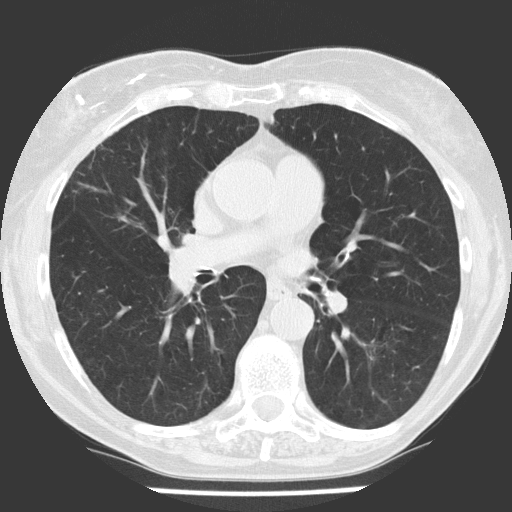
Axial slice from a low-dose chest CT screening exam. Baseline annual screen. Lung window (W 1500 / L -600 HU). Slice 70 of 147 in the series. Female, age 68 years at enrolment.
Expert reader's lesion annotation, bounding box [x1, y1, x2, y2] px = [353, 328, 400, 379]. No non-calcified nodule or mass ≥4 mm was recorded by the screening reader at this exam. Official screen result: negative screen, significant abnormalities not suspicious for lung cancer. Later outcome: lung cancer diagnosed 895 days after this screen — non-small cell carcinoma, left lower lobe, poorly differentiated (G3), stage IA (AJCC 6th edition), 10 mm at pathology.